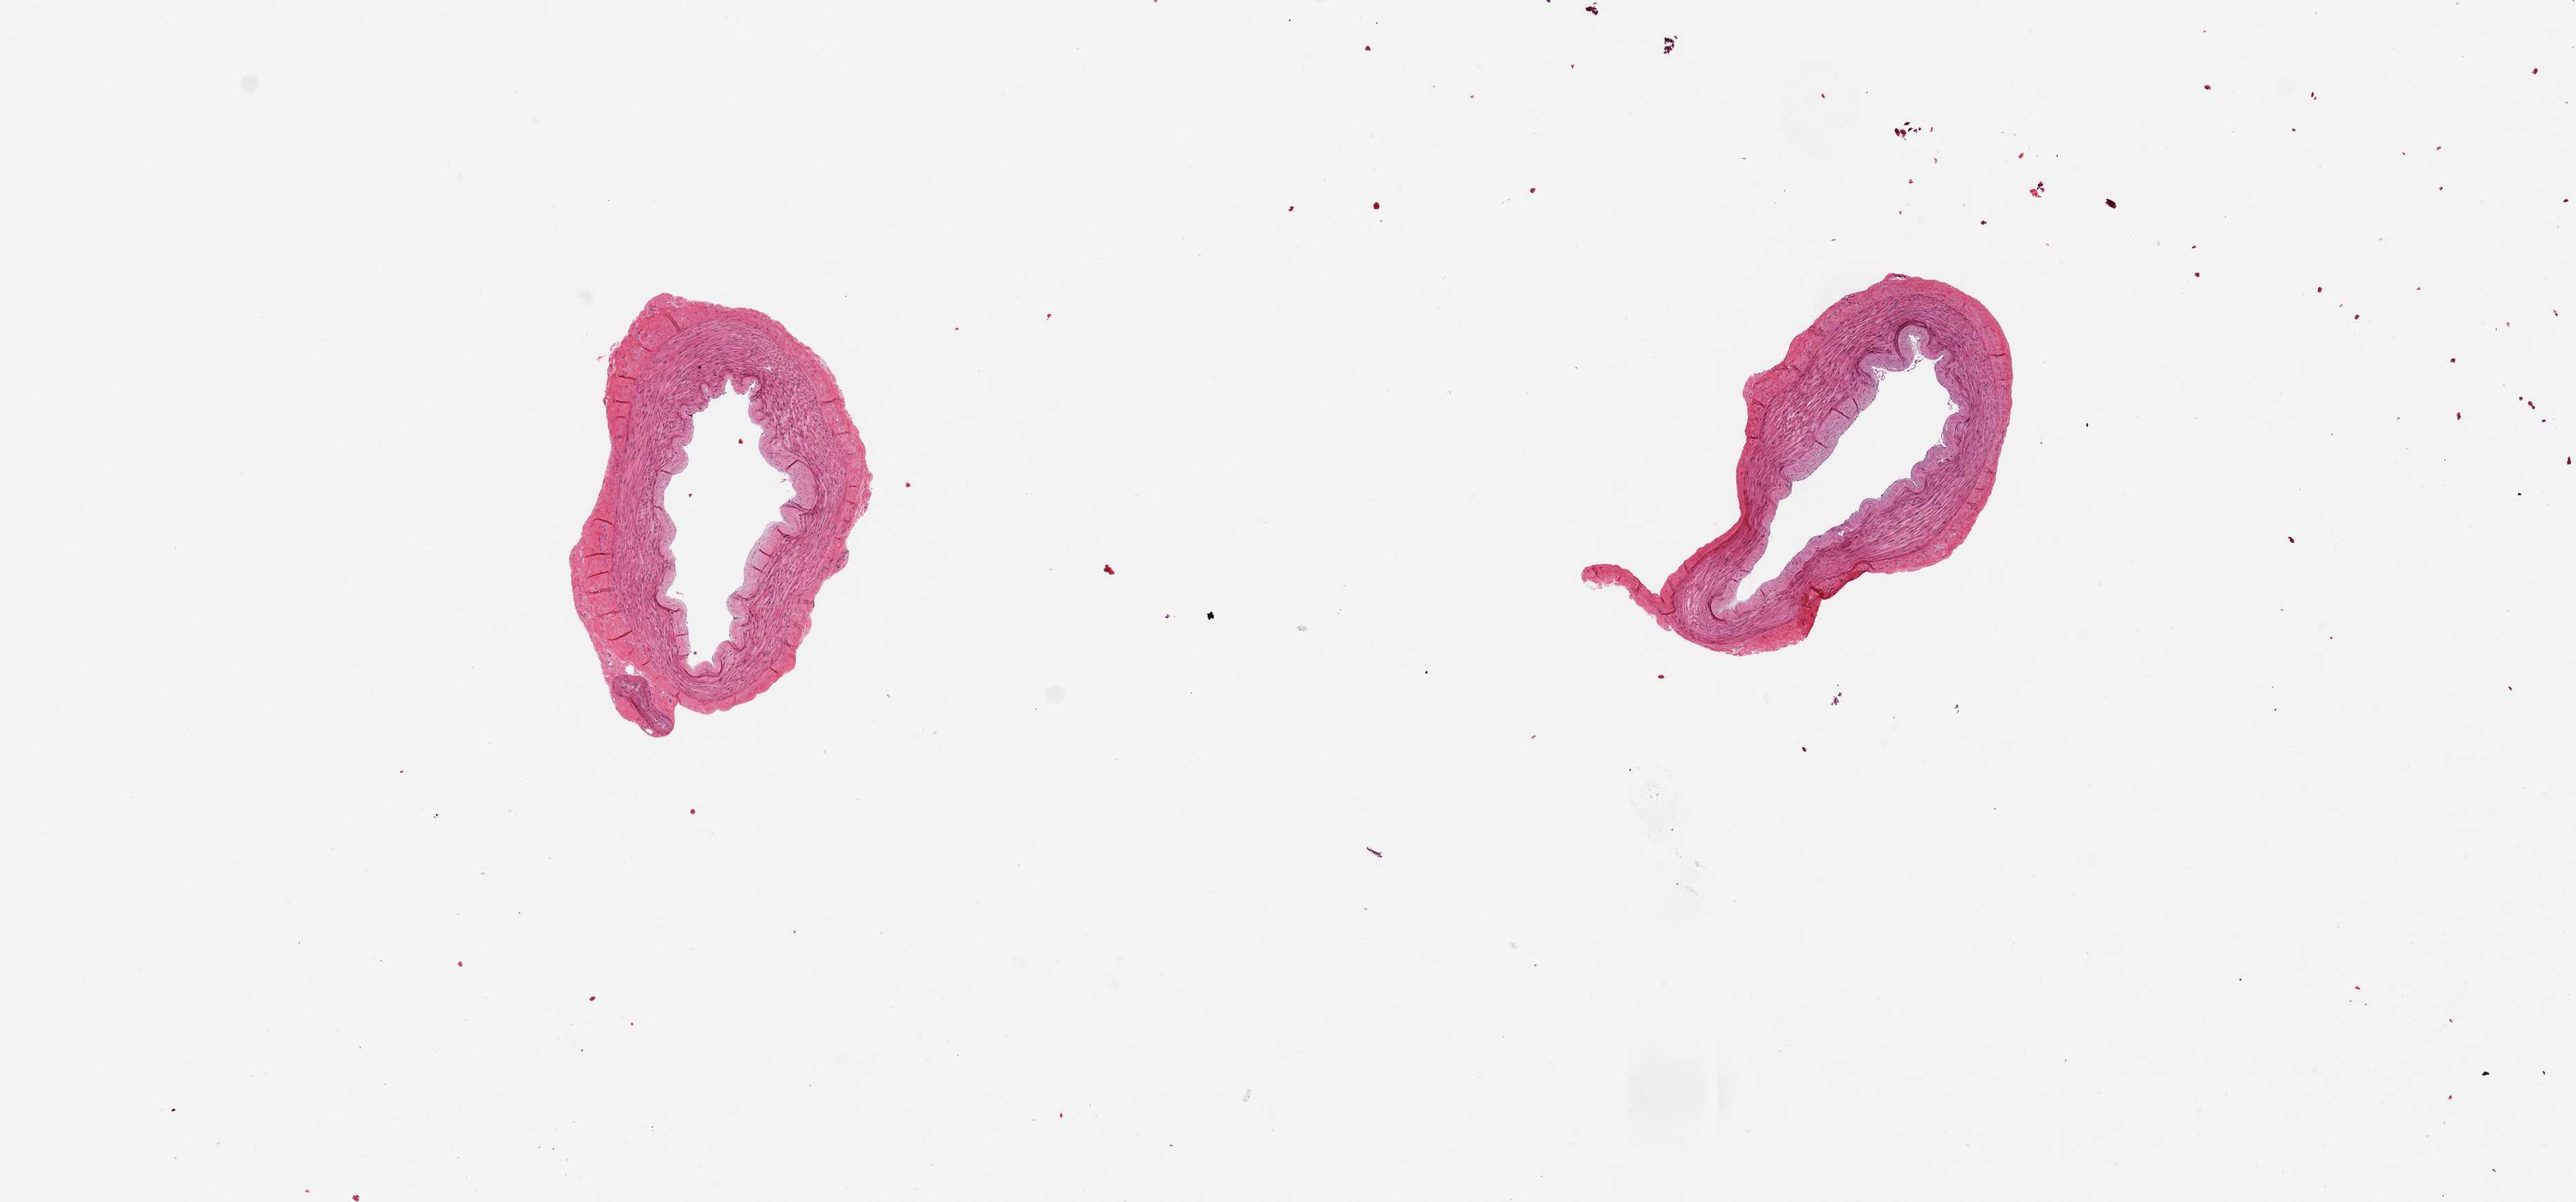
Whole-slide image, haematoxylin and eosin stain — shown as a low-resolution overview of the whole scanned area (about 14.8 x 6.9 mm). PAXgene-fixed, paraffin-embedded tissue. Target tissue: tibial artery. Donor tissue sample. Male donor.
Pathologist's review note for this sample: 2 pieces, 2.5x2 & 2x1.5mm; good clean specimens.